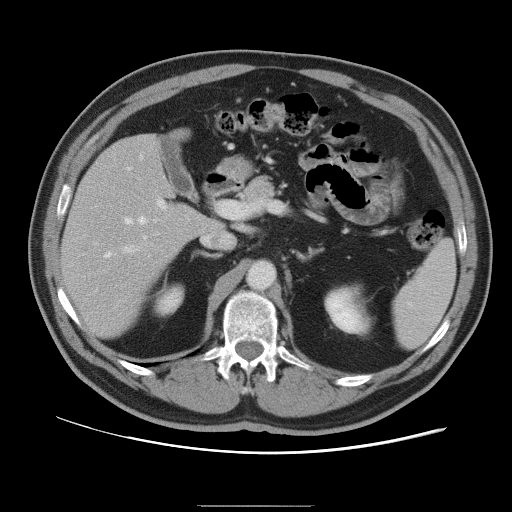
Contrast-enhanced abdominal CT, one axial slice; position 56 of 105 along the scan axis; 120 kVp; intravenous contrast given; soft-tissue window (W 400 / L 40 HU); 512 × 512 image matrix. Male patient, age 64 years. From the clinical record (not read from this slice): diagnosis: colorectal cancer liver metastases, imaged before liver resection; multiple liver metastases: yes; largest metastasis: 3 cm; disease in both lobes: yes.
Annotated regions visible in this slice (outlined manually by an expert reader):
- hepatic veins: bounding box [x1, y1, x2, y2] px = [105, 167, 146, 257]
- liver: [63, 135, 215, 338]
- planned liver remnant (the part of the liver to remain after resection): [63, 135, 215, 338]
- portal vein (with intrahepatic branches): [123, 198, 167, 297]